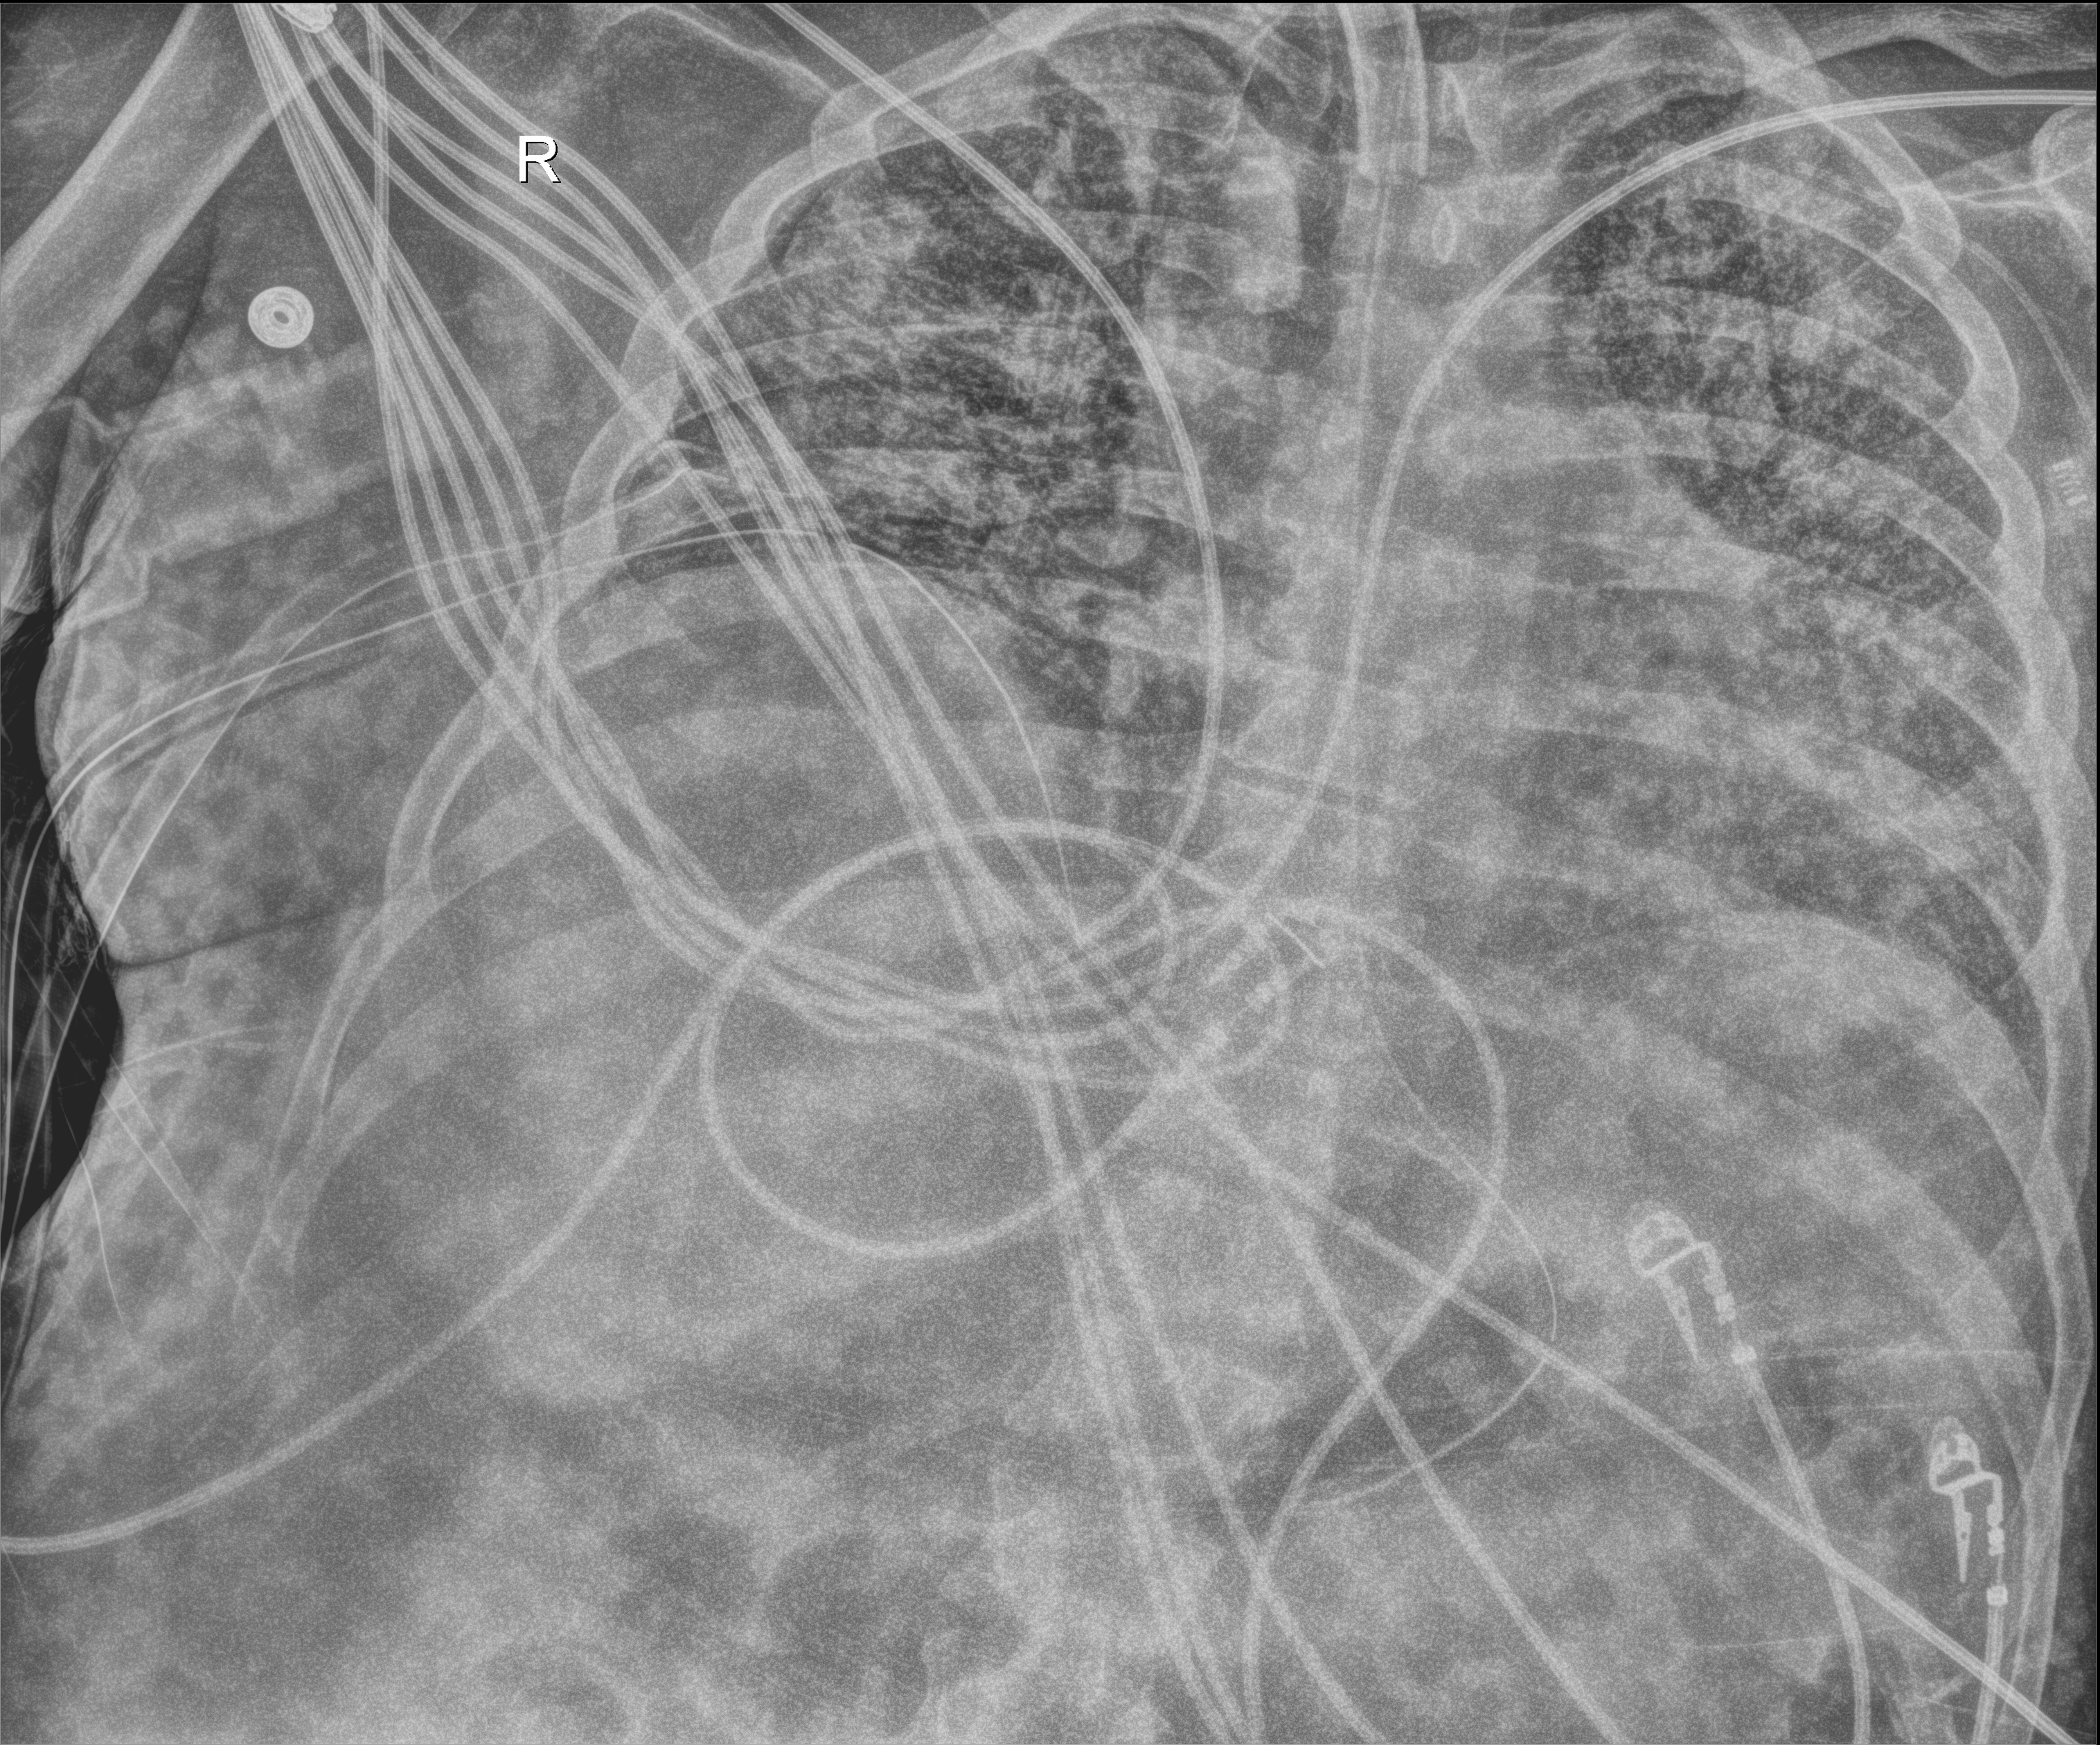
Chest radiograph. Male patient hospitalised with COVID-19, age 18–59 years.
Admission-level facts for this patient (not findings on this image; timing relative to this image not recorded): smoking status (admission record): never.